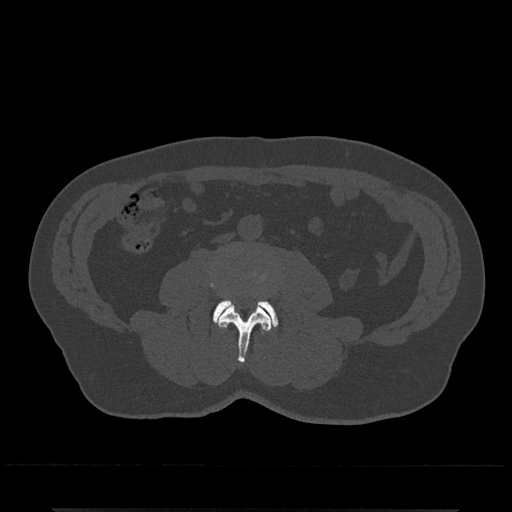
CT including the spine, one axial slice. Position 197 of 797 along the scan axis. 120 kVp. Bone window (W 1800 / L 400 HU). 0.5 mm slice thickness. 512 × 512 image matrix, field of view 393 × 393 mm. Male patient, age 67 years. Case-level facts recorded for this patient, not image findings: primary cancer: prostate.
Structures marked on this image (semi-automatically segmented with operator editing):
- L3 vertebra: bounding box <210,273,272,363> (left, top, right, bottom; pixels)
- L4 vertebra: <213,299,278,326>